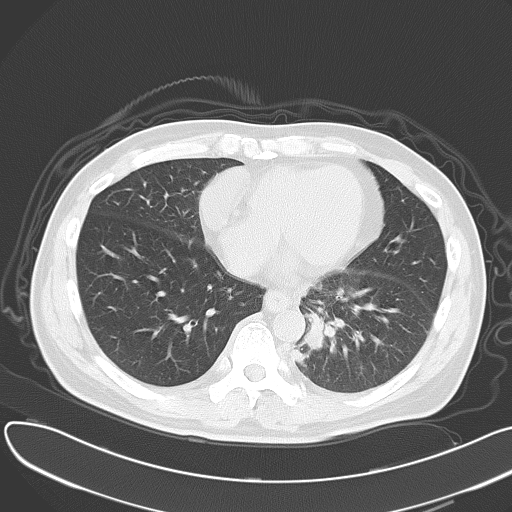
Chest CT, one axial slice; slice 18 of 55 in the series (ordered by position); 120 kVp; lung window (W 1500 / L -600 HU); 5 mm slice thickness; 512 × 512 image matrix, field of view 376 × 376 mm. Male patient, age 55 years. Case-level facts recorded for this patient, not image findings: clinical TNM (as recorded): T2 N3 M0; histopathological grade: G3.
Annotated regions visible in this slice (rectangle marked by the reading radiologist):
- lung tumour (recorded histology: small cell carcinoma): bounding box (x1, y1, x2, y2) in pixels: (300, 311, 336, 361)